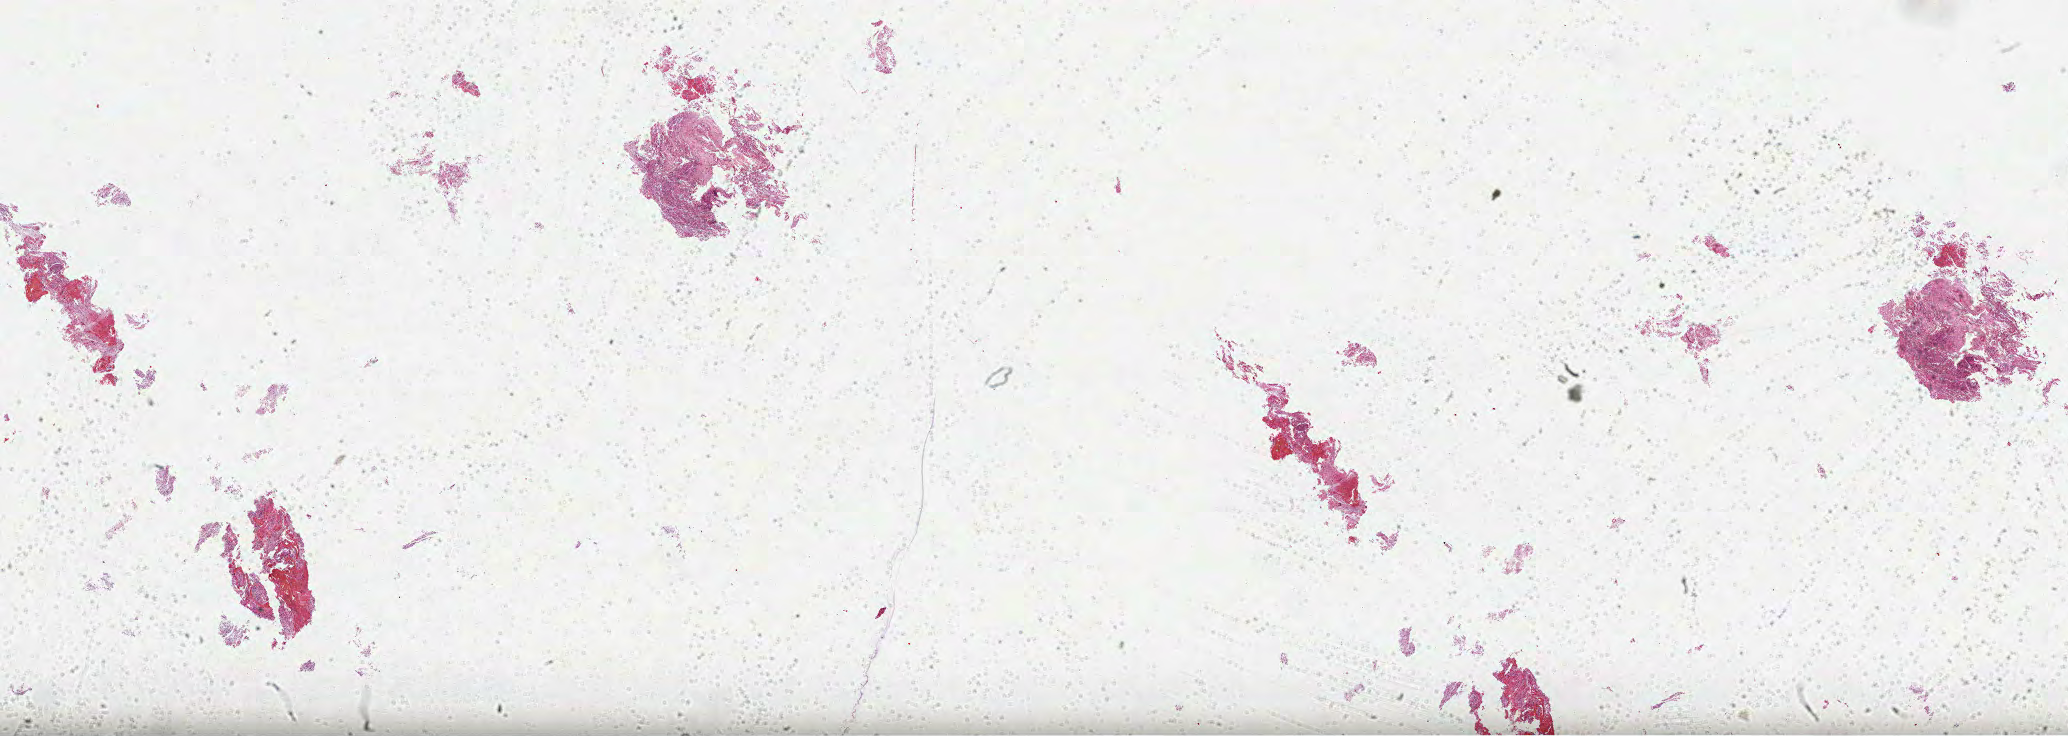
Whole-slide histology image, H&E-stained, shown as a low-resolution overview of the whole scanned area (about 33.4 x 11.9 mm, from a 40x scan); formalin-fixed paraffin-embedded (FFPE) diagnostic section; brain, primary tumour sample. Male patient; age at initial diagnosis 89 years.
Diagnosis: Glioblastoma.